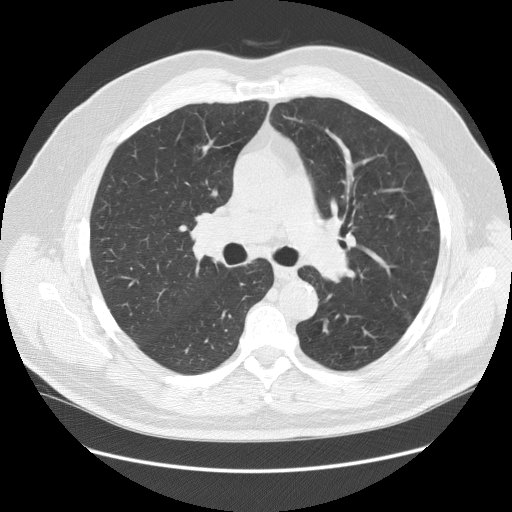
Axial slice from a low-dose chest CT screening exam; baseline annual screen; lung window (W 1500 / L -600 HU); 2.5 mm slice thickness; standard (soft-tissue) reconstruction kernel (STANDARD); 512 × 512 image matrix, field of view 400 × 400 mm. Male participant, aged 64 years at enrolment. Former smoker at enrolment.
Expert reader's lesion annotation, bounding box <180,198,248,269> (left, top, right, bottom; pixels). Reader record for this screening exam (exam-level; its link to the box is not recorded): non-calcified nodule or mass ≥4 mm, right lower lobe, 7 × 5 mm, smooth margins, soft tissue attenuation. Participant outcome: lung cancer diagnosed 456 days after this screen (after the second annual screen) — adenocarcinoma, NOS, right upper lobe, poorly differentiated (G3), stage IB (AJCC 6th edition), 37 mm at pathology.